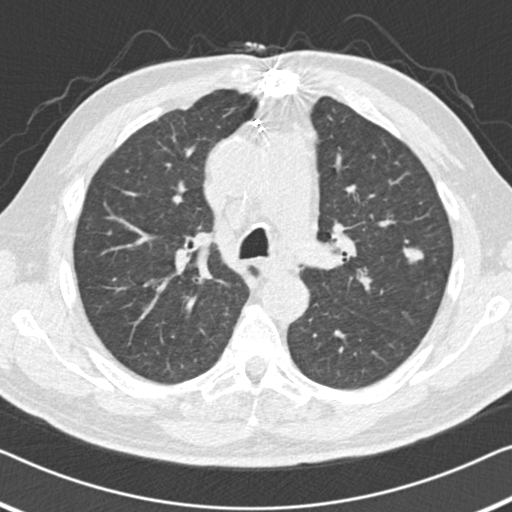
Low-dose screening chest CT, axial slice, baseline annual screen, lung window (W 1500 / L -600 HU), standard (soft-tissue) reconstruction kernel (B30f), 120 kVp. Male participant, aged 64 years at enrolment.
Expert-annotated lung lesion, bounding box [x1, y1, x2, y2] px = [387, 229, 442, 279]. The screening reader recorded 2 non-calcified nodules or masses ≥4 mm on this exam; which of them this box marks is not recorded. Official screen result: positive, change unspecified: nodule(s) >= 4 mm or enlarging nodule(s), mass(es), or other non-specific abnormalities suspicious for lung cancer. Participant outcome: lung cancer diagnosed 133 days after this screen — adenocarcinoma, NOS, left upper lobe, poorly differentiated (G3), stage IA (AJCC 6th edition), 15 mm at pathology.